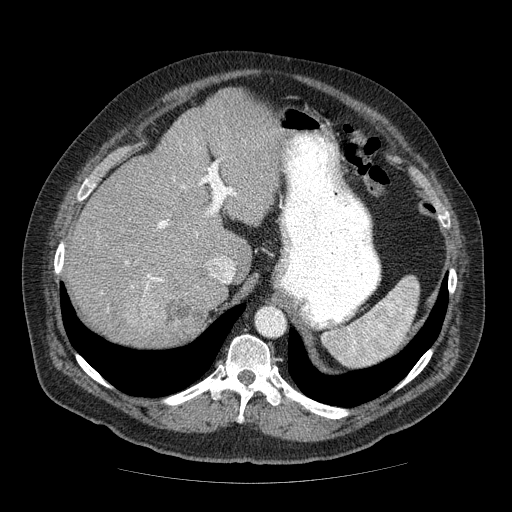
Contrast-enhanced abdominal CT (liver protocol), one axial slice. Slice 46 of 85 in the series (ordered by position). Reconstruction kernel STANDARD. Soft-tissue window (W 400 / L 40 HU). 2.5 mm slice thickness. 512 × 512 image matrix. Case-level facts recorded for this patient, not image findings: diagnosis: hepatocellular carcinoma (patient treated with transarterial chemoembolisation; whether this scan precedes or follows treatment is not stated here); TNM stage (as recorded): Stage-IIIA; Child-Pugh class: A; tumour nodularity: multinodular; tumour size: 7 cm.
Structures marked on this image (semi-automatic segmentation, software-assisted and operator-edited):
- liver parenchyma outside the tumour (the mass and vessels are separate outlines, so this box may not span the whole liver): bounding box [x1, y1, x2, y2] px = [66, 88, 282, 344]
- mass: [127, 282, 215, 348]
- liver vessels: [125, 178, 236, 290]